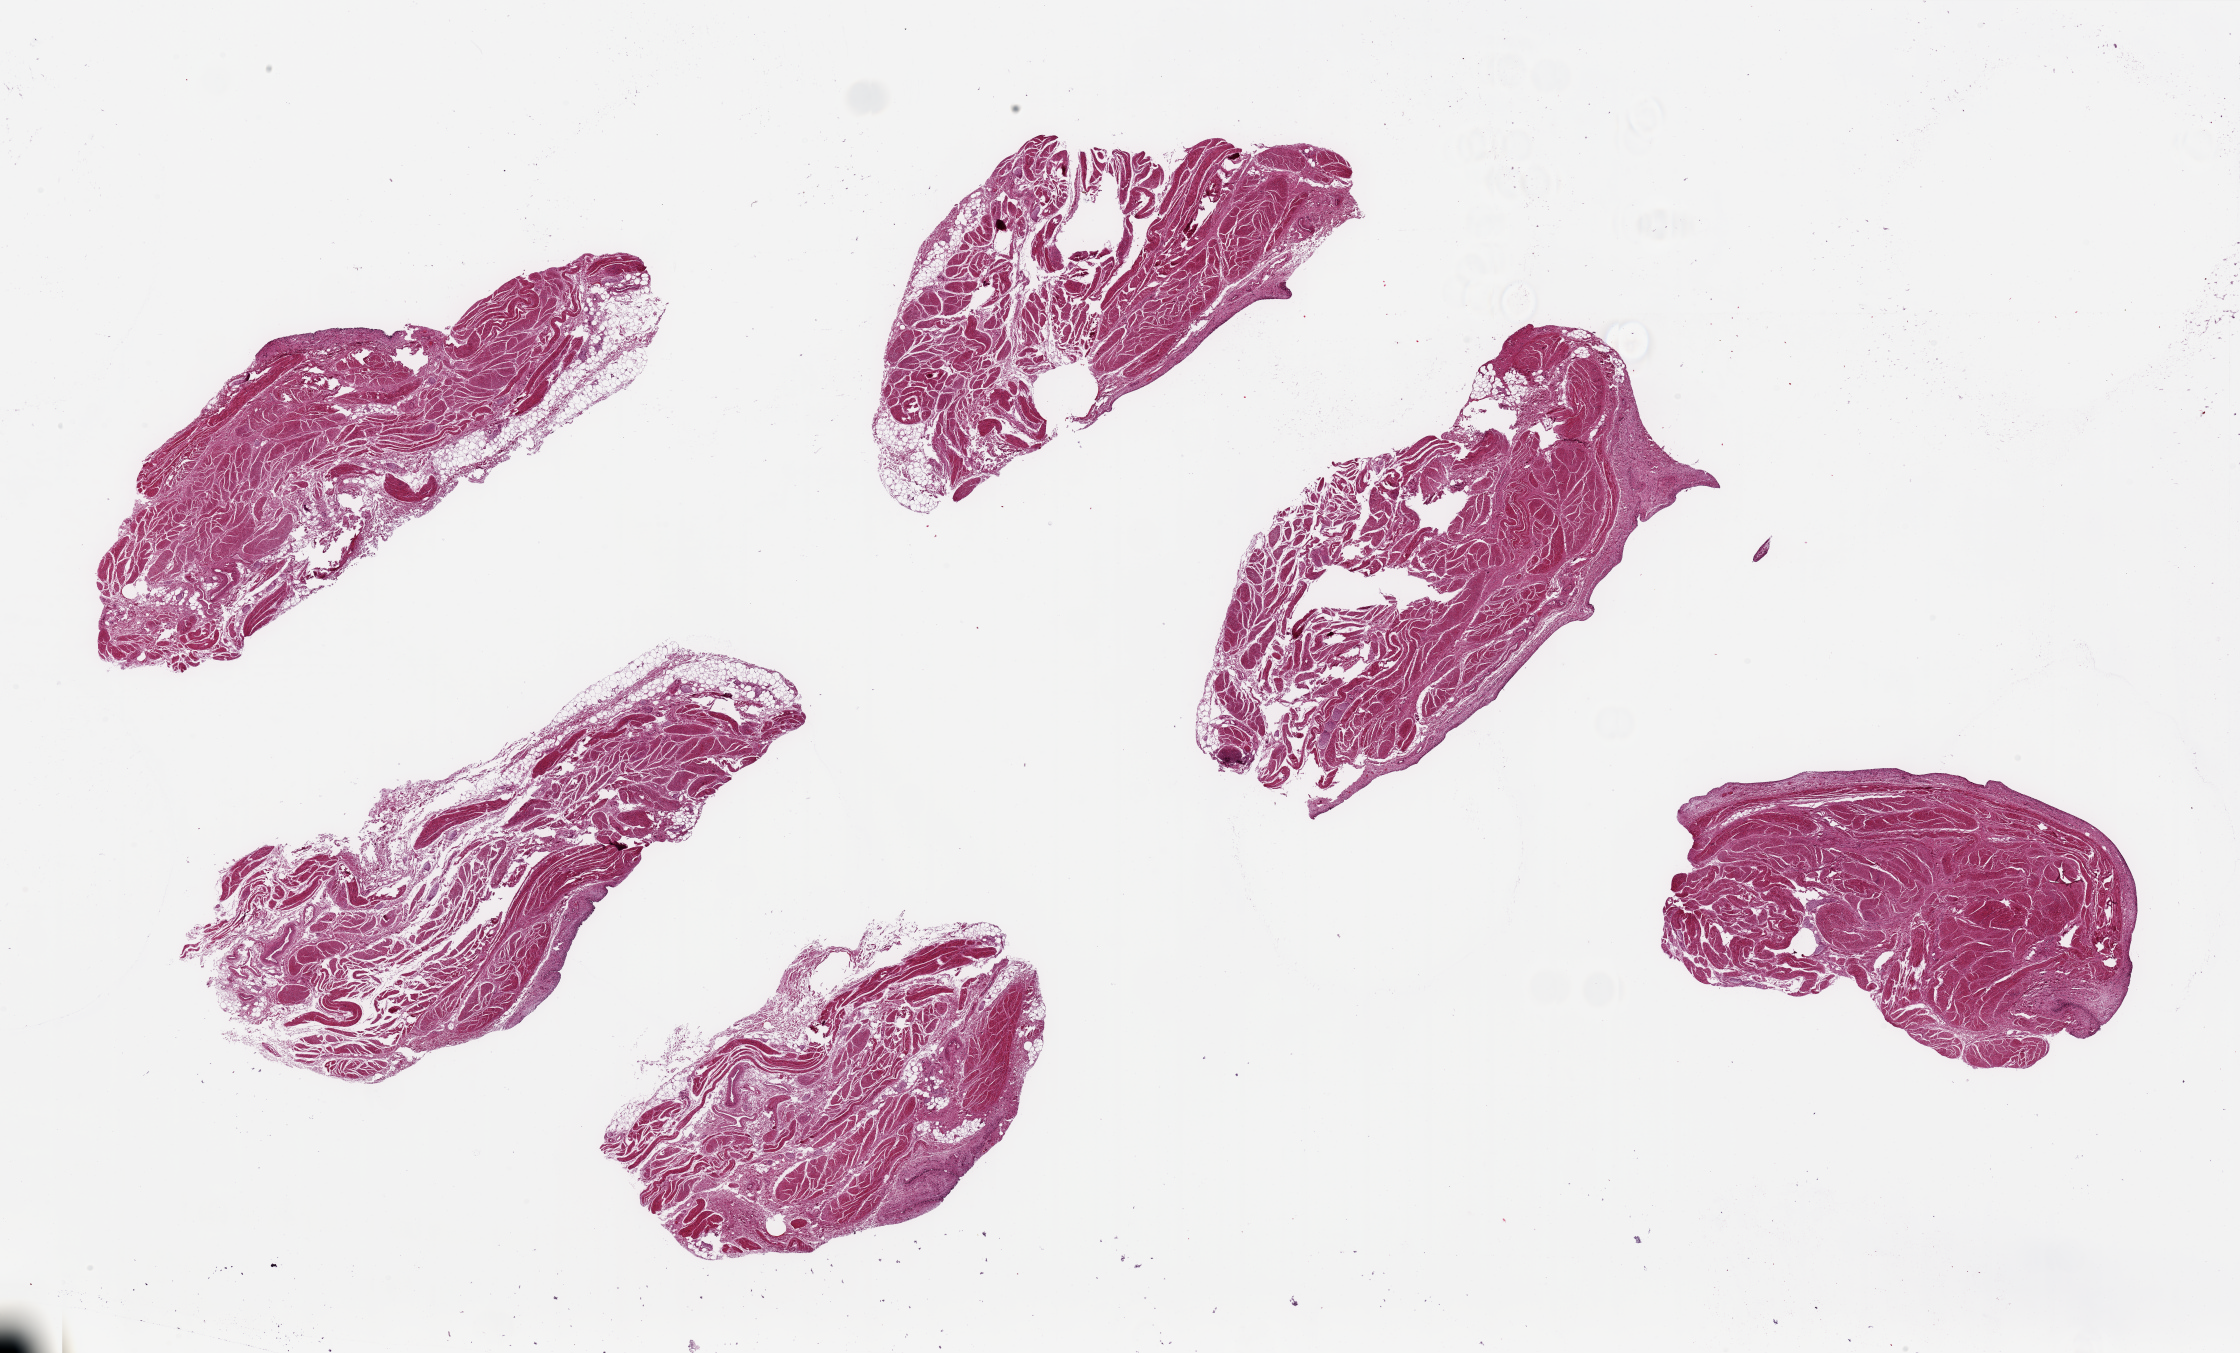
Haematoxylin and eosin whole-slide image, low-resolution overview of the scanned area, about 35.4 x 21.4 mm, PAXgene-fixed paraffin-embedded (PFPE) section, target tissue: urinary bladder, tissue donor sample. Donor: male.
Review note (as recorded): 6 ~8x4mm pieces. Urothelium totally sloughed, areas of poor fixation with tears/holes.